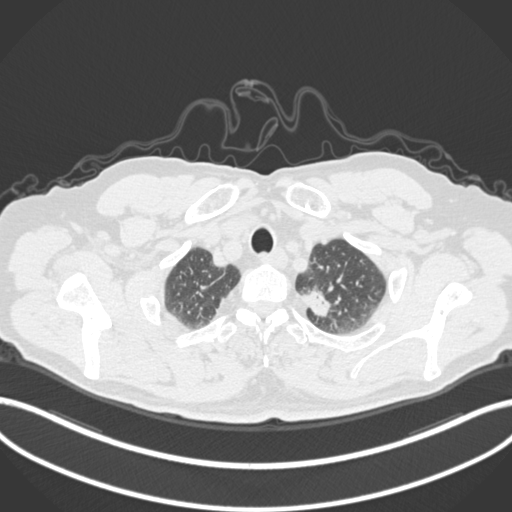
Chest CT, one axial slice. Slice 286 of 306 in the series (ordered by position). Reconstruction kernel B30f. Lung window (W 1500 / L -600 HU). 1 mm slice thickness. 512 × 512 image matrix, field of view 400 × 400 mm. Male patient, age 64 years. From the clinical record (not read from this slice): clinical TNM (as recorded): T1c N0 M0.
Structures marked on this image (bounding box drawn by a radiologist):
- lung tumour (recorded histology: adenocarcinoma): bounding box [x1, y1, x2, y2] px = [299, 281, 336, 323]